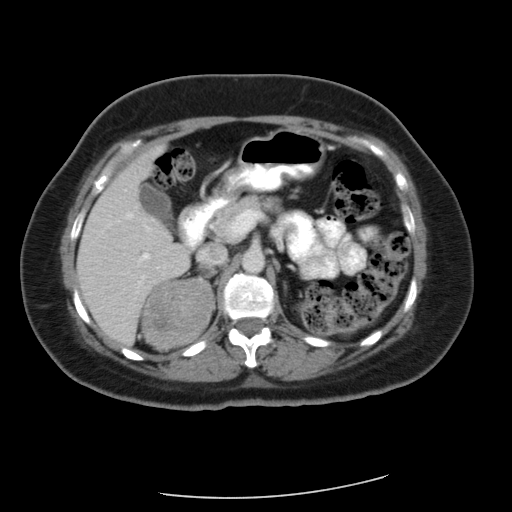
Contrast-enhanced abdominal CT, one axial slice. Slice 35 of 56 in the series (ordered by position). Soft-tissue window (W 400 / L 40 HU). 5 mm slice thickness. 512 × 512 image matrix, field of view 400 × 400 mm. Patient: female, 58 years. Case-level facts recorded for this patient, not image findings: diagnosis: adrenocortical carcinoma; tumour side: right adrenal.
Structures marked on this image (semi-automatic segmentation, software-assisted and operator-edited):
- mass: bounding box [x1, y1, x2, y2] px = [143, 279, 215, 350]